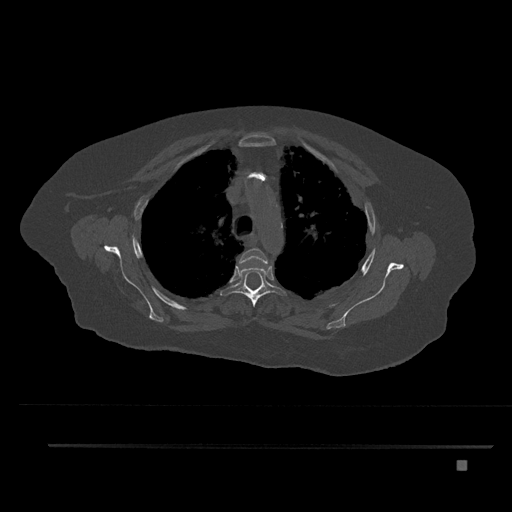
CT including the spine, one axial slice; slice 609 of 797 in the series (ordered by position); bone window (W 1800 / L 400 HU); 512 × 512 image matrix, field of view 437 × 437 mm. Patient: female, 76 years. Case-level facts recorded for this patient, not image findings: primary cancer: lung; vertebrae with lytic lesions (as recorded): T11, L3.
Annotated regions visible in this slice (semi-automatically segmented with operator editing):
- T3 vertebra: bounding box [x1, y1, x2, y2] px = [239, 248, 268, 266]
- T4 vertebra: [220, 258, 286, 306]